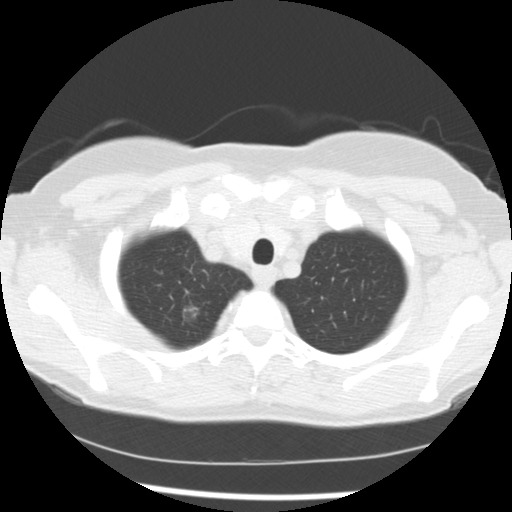
Chest CT (low-dose screening protocol), one axial image. First (baseline) screen. Lung window (W 1500 / L -600 HU). 2.5 mm slice thickness. Standard (soft-tissue) reconstruction kernel (STANDARD). Slice 23 of 241 in the series. Female, age 60 years at enrolment.
Expert reader's lesion annotation, box from (x=168, y=292) to (x=211, y=330) px. The screening reader recorded 3 non-calcified nodules or masses ≥4 mm on this exam (right upper lobe, right middle lobe, left lower lobe); which of them this box marks is not recorded. Later outcome: lung cancer diagnosed 100 days after this screen — bronchiolo-alveolar adenocarcinoma, NOS, right upper lobe, moderately differentiated (G2), stage IA (AJCC 6th edition), 9 mm at pathology.